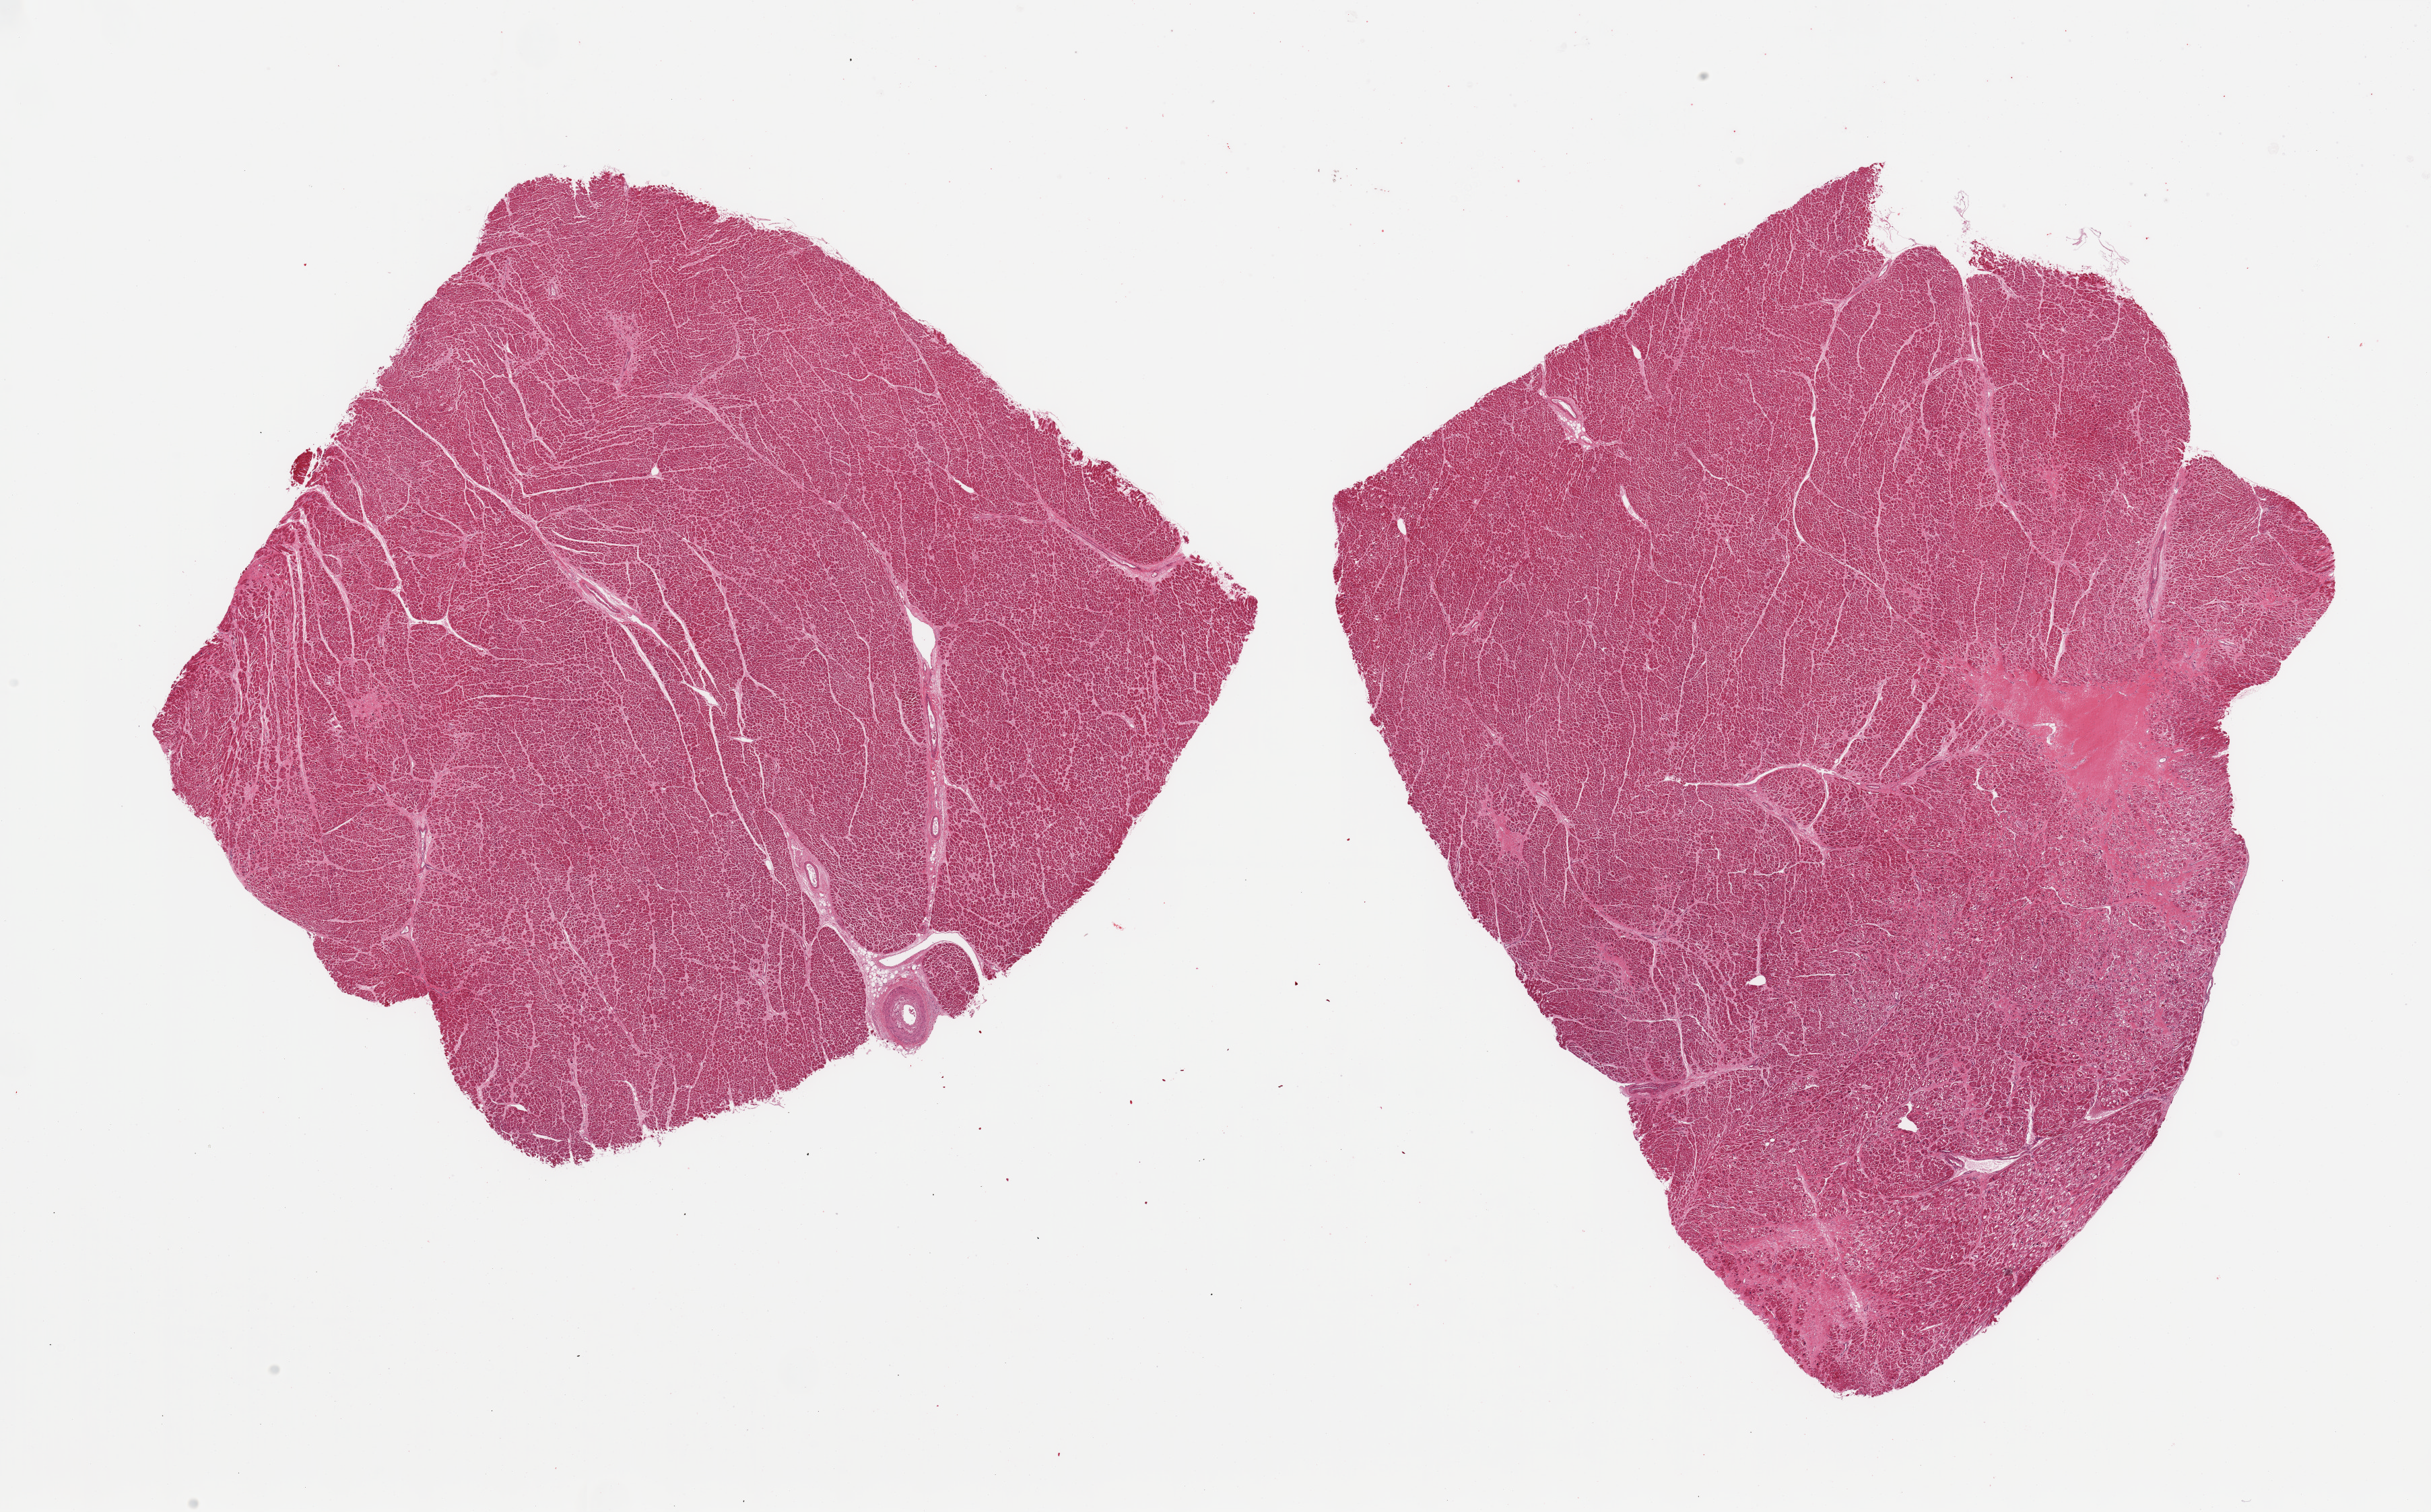
Haematoxylin and eosin whole-slide image — low-resolution overview of the scanned area, about 28.5 x 17.8 mm; PAXgene-fixed paraffin-embedded (PFPE) section; section of heart (target tissue); tissue donor sample.
Review note (as recorded): 2 pieces; mild patchy fibrosis; 0.8mm coronary artery included.